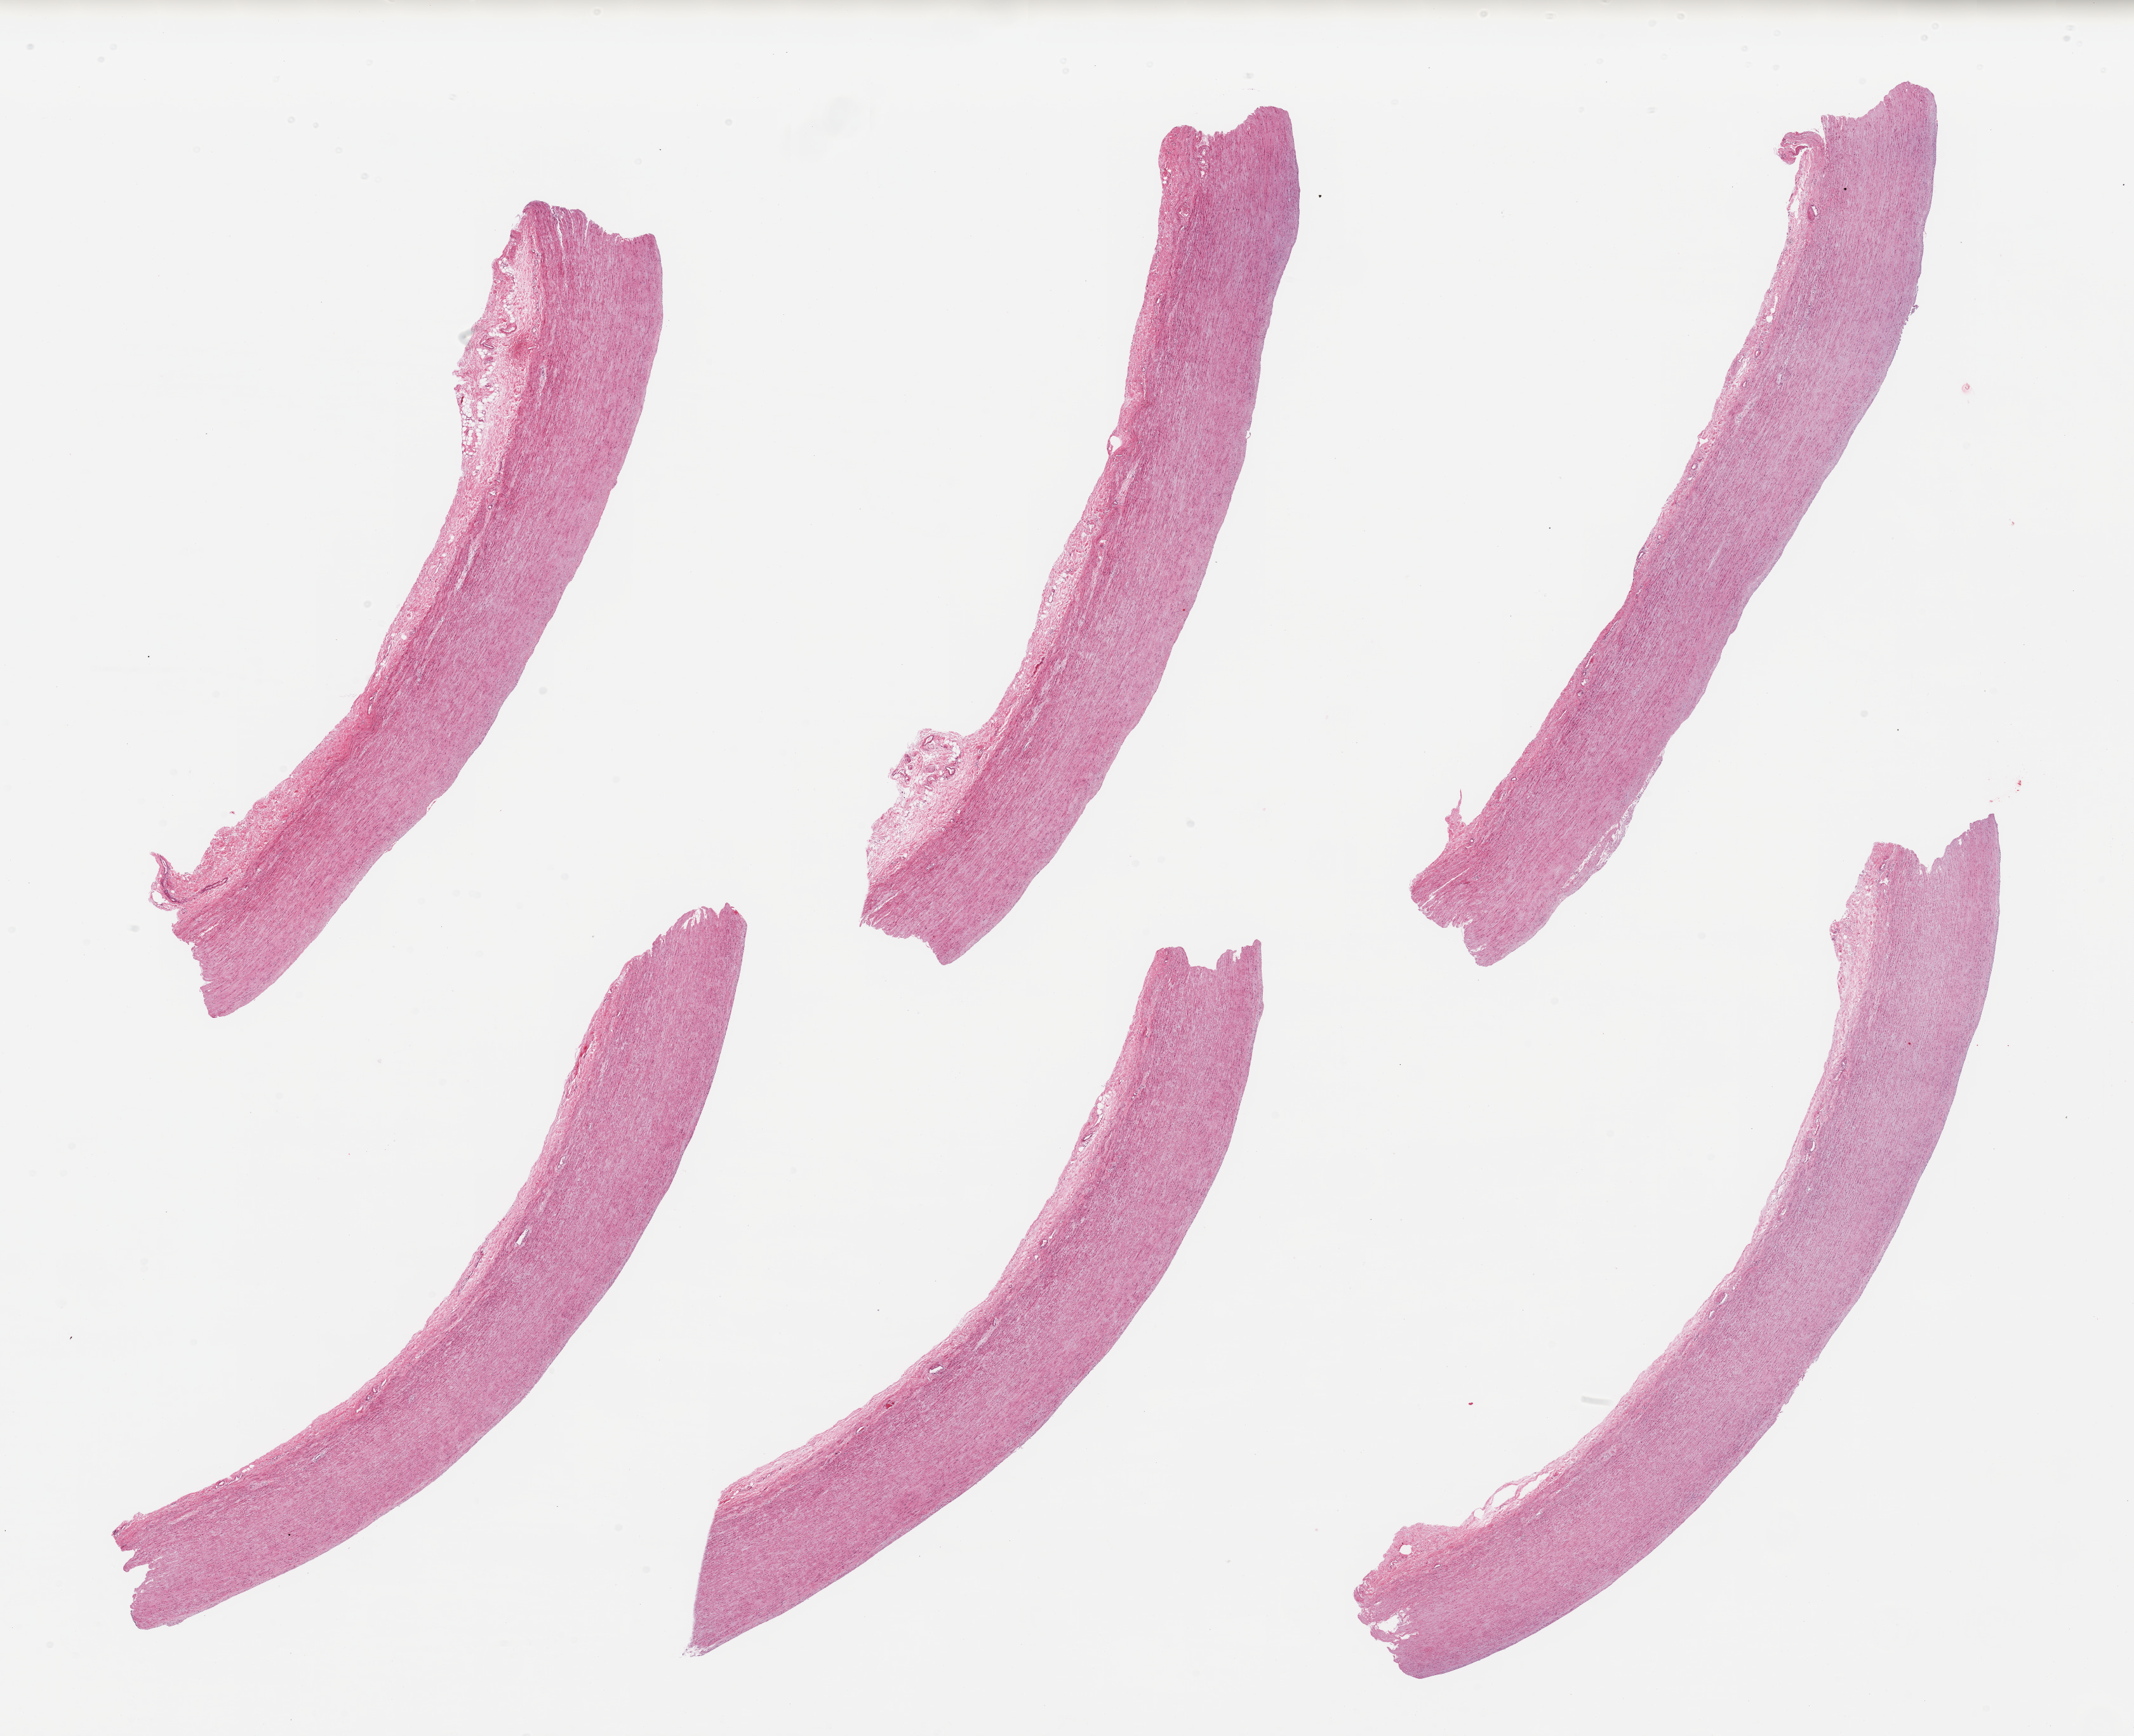
Haematoxylin and eosin whole-slide image, shown as a low-resolution overview of the whole scanned area (about 26.6 x 21.6 mm, slide scanned at 20x). PAXgene-fixed paraffin-embedded (PFPE) section. Sampled site (target tissue): aorta. Donor tissue sample. Donor sex: male.
Review note (as recorded): 6 pieces; minimal fibrous intimal thickening; well dissected.